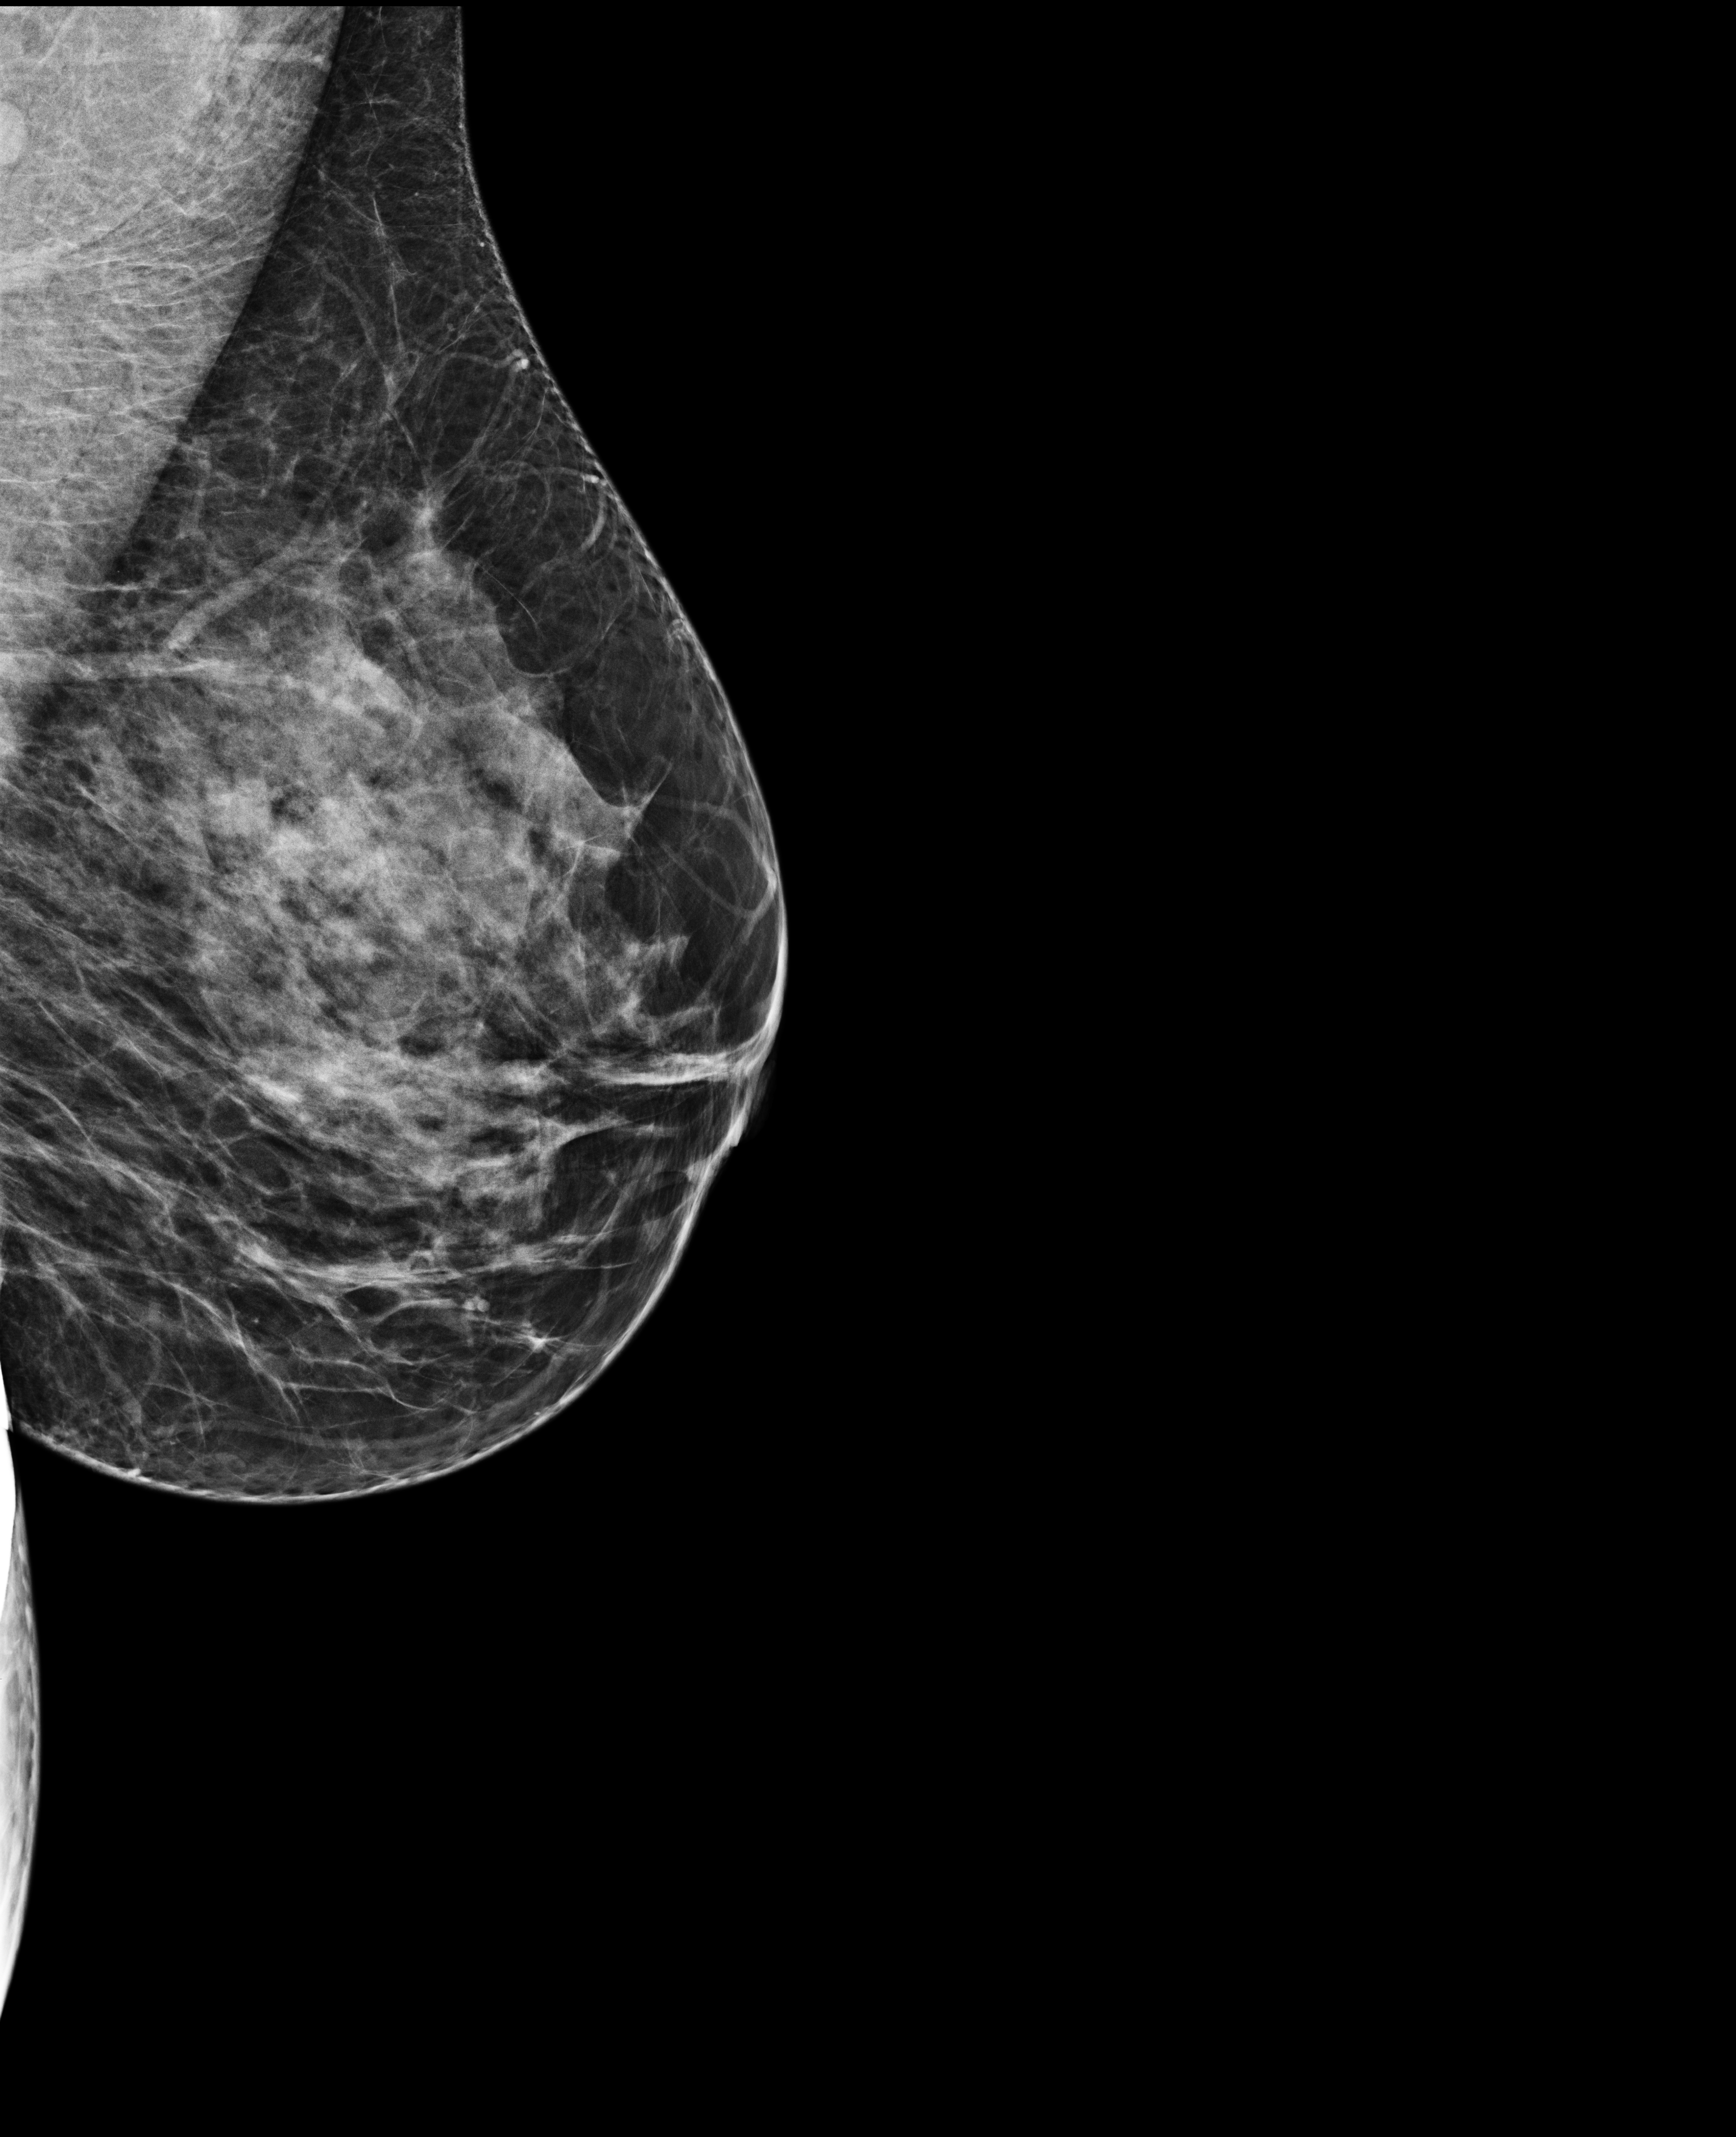
Digital mammogram (FFDM), right breast, MLO view, annual screening mammography examination, compressed breast thickness 57 mm, system: Selenia Dimensions. Female patient, age 48 years.
Final BI-RADS assessment for this screening round (tomosynthesis exam, both breasts): category 1.